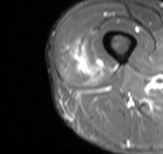
MRI of an extremity soft-tissue mass, one axial slice; position 13 of 61 along the scan axis; STIR; MR volume resampled by the dataset authors to the PET/CT grid (not the native acquisition matrix); 3.27 mm slice thickness; 163 × 154 image matrix, field of view 159 × 150 mm. Male patient. Case-level facts recorded for this patient, not image findings: histological type: poorly differentiated synovial sarcoma; grade: high; site of the primary tumour: right buttock.
Structures marked on this image (expert contour drawn on MRI and transferred to this co-registered scan by the dataset authors):
- gross tumour volume including surrounding oedema: box from (x=71, y=41) to (x=101, y=74) px